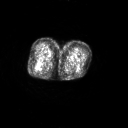
FDG PET of an extremity soft-tissue mass (from a PET/CT study), one axial slice. Slice 24 of 267 in the series (ordered by position). 3.27 mm slice thickness. 128 × 128 image matrix. Female patient, age 70 years. From the clinical record (not read from this slice): histological type: synovial sarcoma; grade: intermediate; site of the primary tumour: right buttock.
Annotated regions visible in this slice (expert contour drawn on MRI and transferred to this co-registered scan by the dataset authors):
- gross tumour volume including surrounding oedema: bounding box <35,60,39,69> (left, top, right, bottom; pixels)